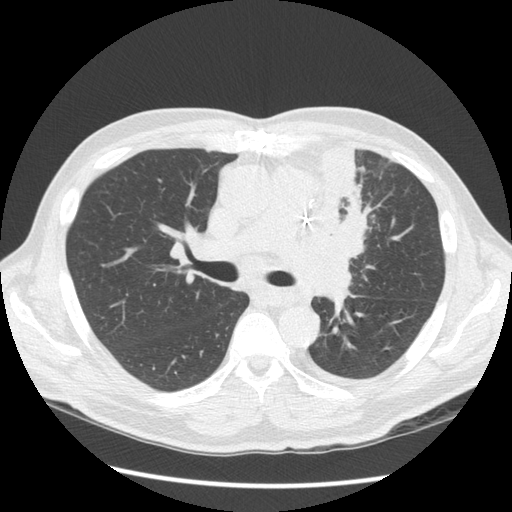
Low-dose screening chest CT, one axial slice; lung window (W 1500 / L -600 HU); 2.5 mm slice thickness; 512 × 512 image matrix.
Outlined on this slice (outlined manually by an expert reader):
- lesion 1 (tumor, upper lobe of left lung): bounding box <297,145,371,304> (left, top, right, bottom; pixels)